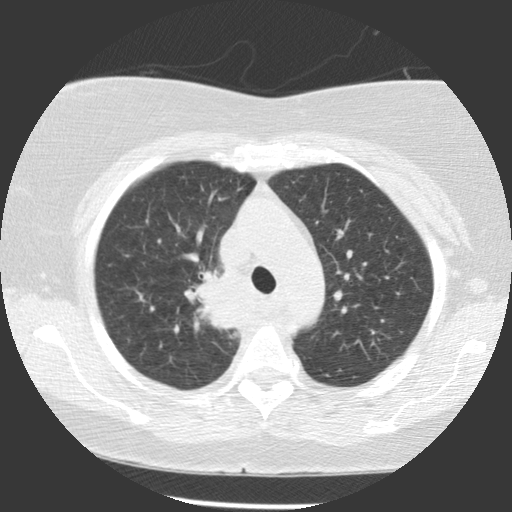
Low-dose screening chest CT, one axial slice. Position 85 of 116 along the scan axis. 140 kVp. Lung window (W 1500 / L -600 HU). 2.5 mm slice thickness. 512 × 512 image matrix.
Outlined on this slice (expert manual segmentation):
- lesion 1 (tumor, upper lobe of right lung): bounding box (x1, y1, x2, y2) in pixels: (196, 273, 246, 330)